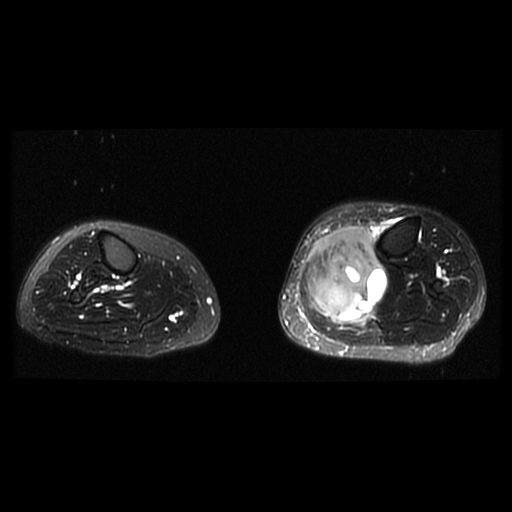
MRI of an extremity soft-tissue mass, one axial slice; slice 15 of 38 in the series (ordered by position); T2-weighted fat-saturated; 6 mm slice thickness; 512 × 512 image matrix, field of view 330 × 330 mm. Female patient. From the clinical record (not read from this slice): histological type: extraskeletal high grade osteogenic sarcoma; grade: high; site of the primary tumour: left calf.
Structures marked on this image (outlined manually by an expert reader):
- gross tumour volume (mass): box from (x=308, y=226) to (x=387, y=321) px